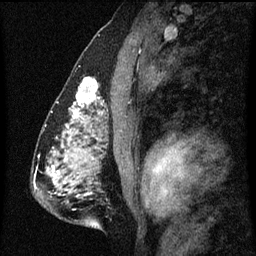
Breast MRI (dynamic contrast-enhanced), one sagittal slice. Position 36 of 60 along the scan axis. Dynamic contrast-enhanced series, image 2 of 3 at this slice position (ordered by acquisition). 1.5 T. TE 4.2 ms, TR 8 ms. 2 mm slice thickness. 256 × 256 image matrix. Patient: female, 51 years.
Outlined on this slice (semi-automatically segmented with operator editing):
- analysis volume of interest (the breast-tissue region the enhancement analysis was run in; not a lesion): box from (x=61, y=78) to (x=102, y=129) px
- tumour enhancement mask (voxels above the 70 % enhancement threshold inside the analysis volume of interest): (x=71, y=78)–(x=102, y=121)